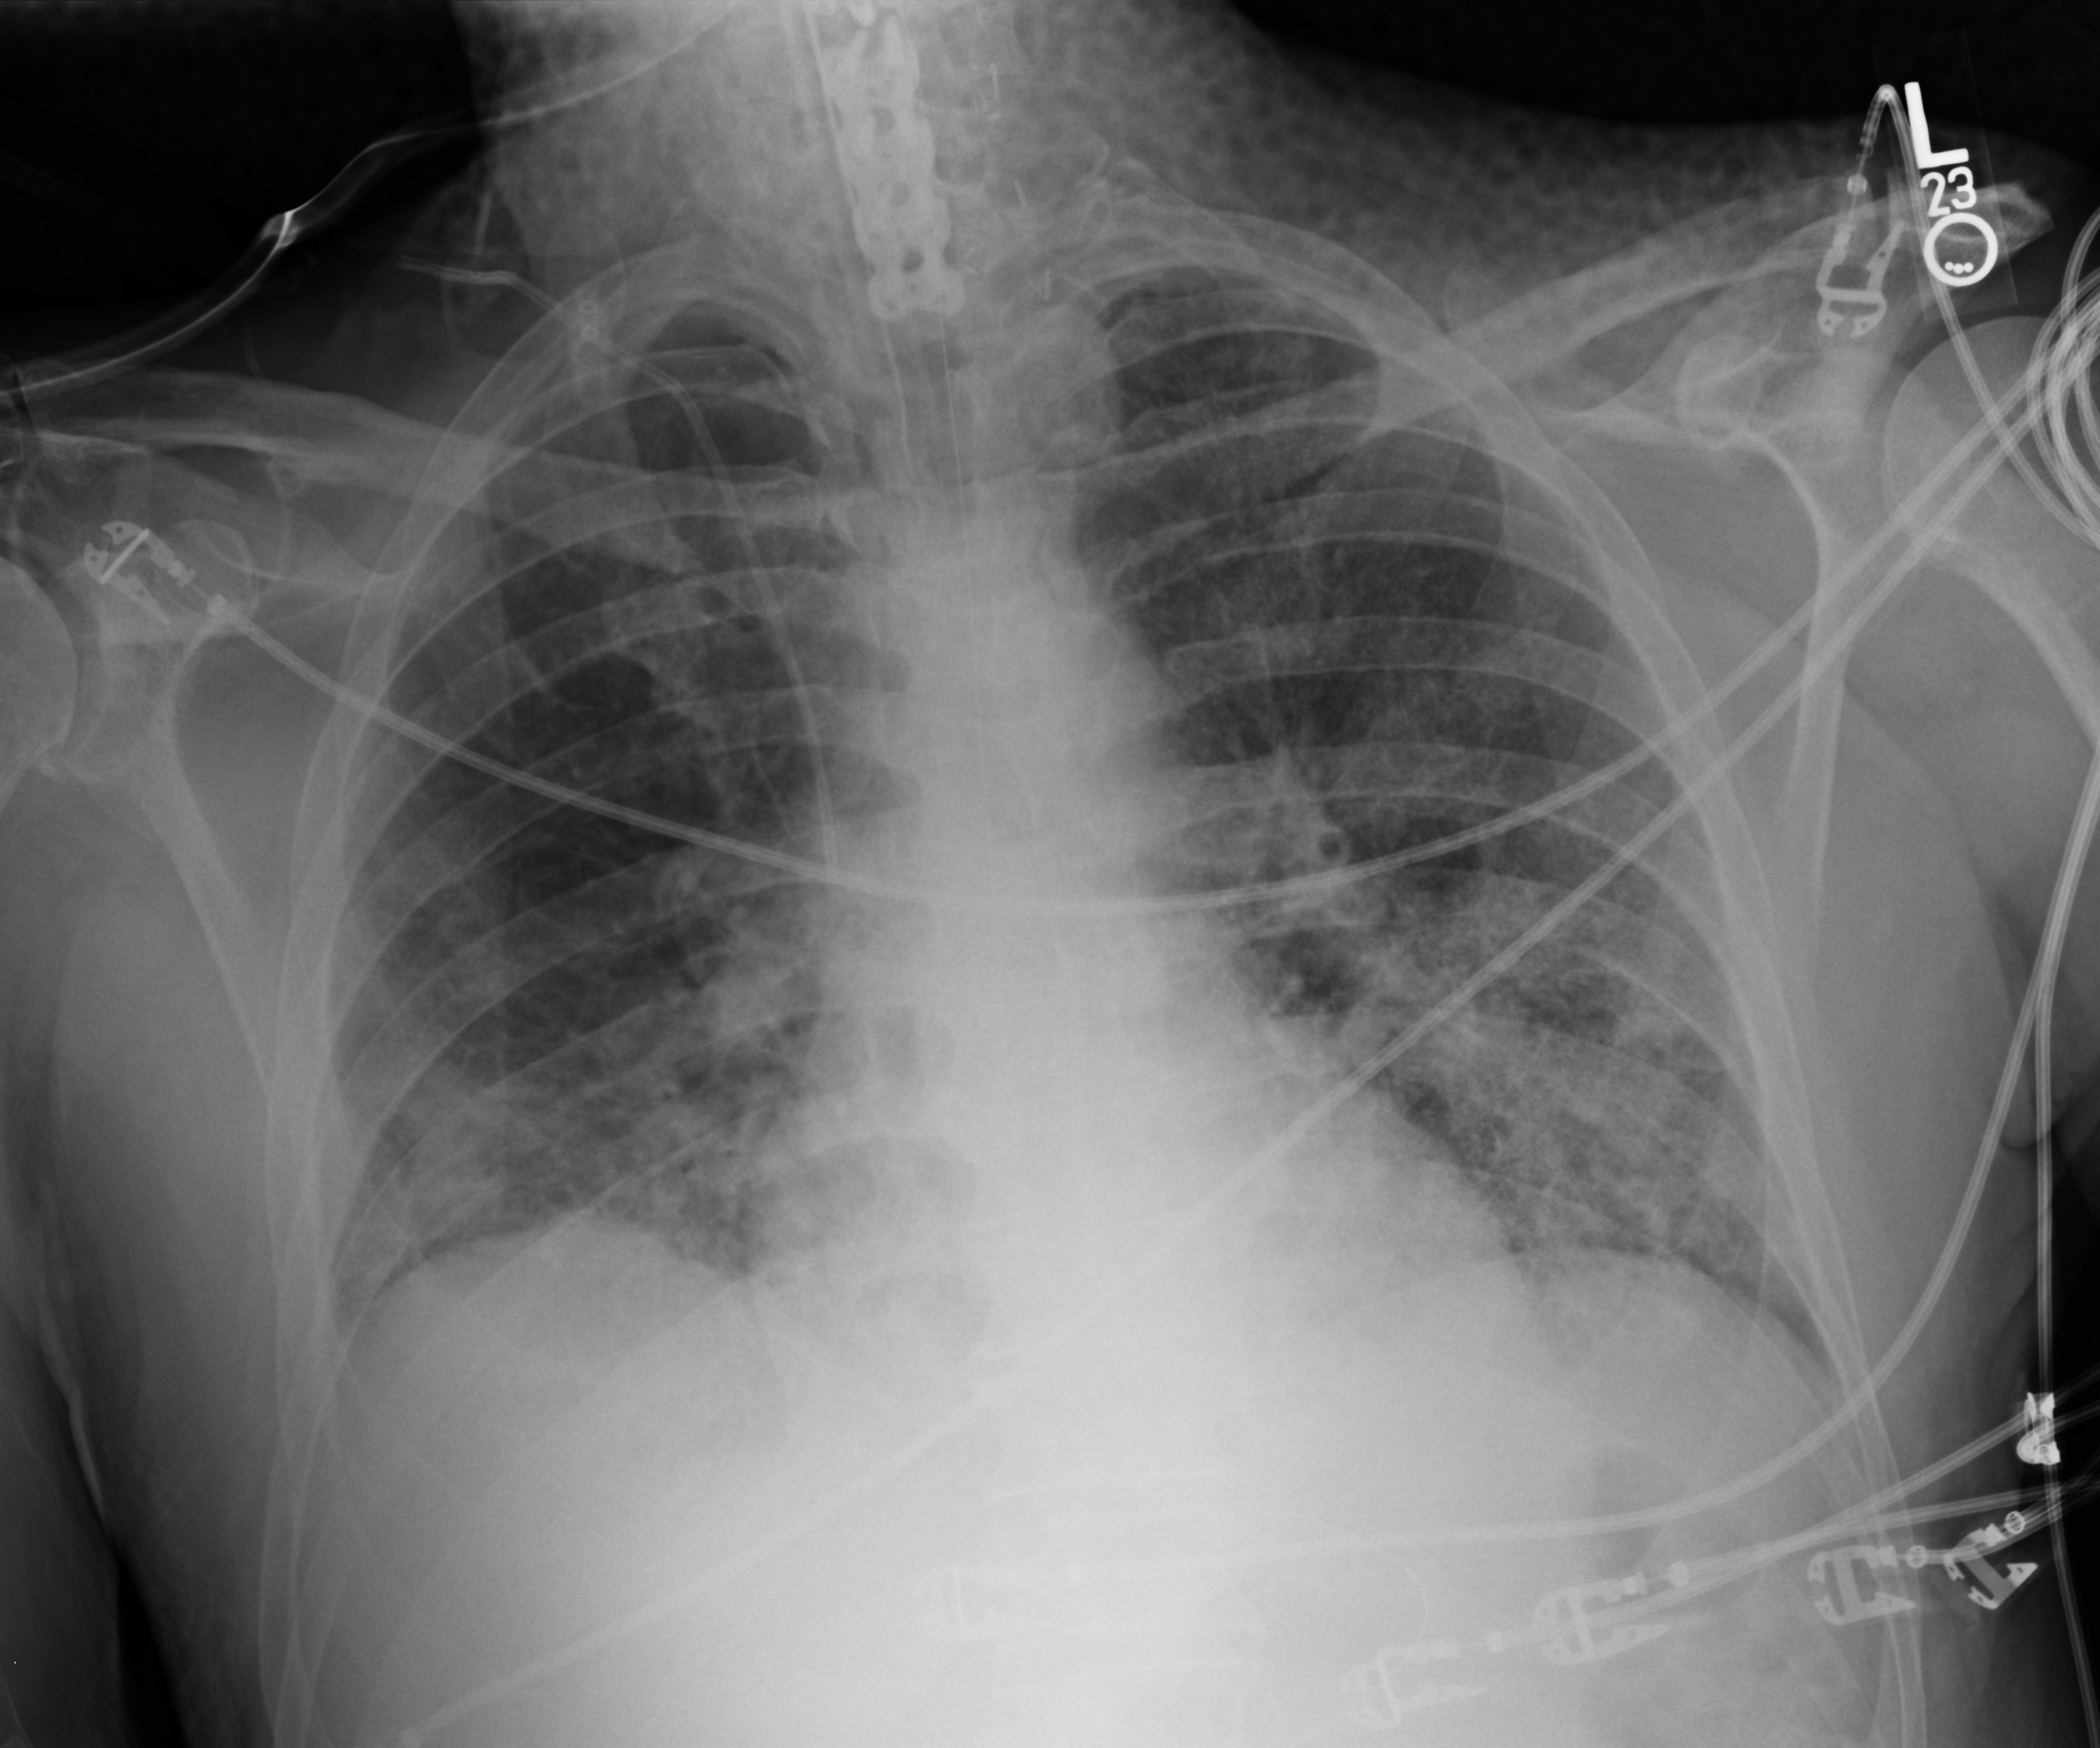
Bedside chest radiograph (computed radiography), anteroposterior (AP) projection. Patient hospitalised with COVID-19; male, aged 60–74 years.
Hospital-stay facts (about this admission, not read from this image; timing relative to this image not recorded):
- mechanically ventilated during this hospital stay: yes
- admitted to intensive care during this hospital stay: yes